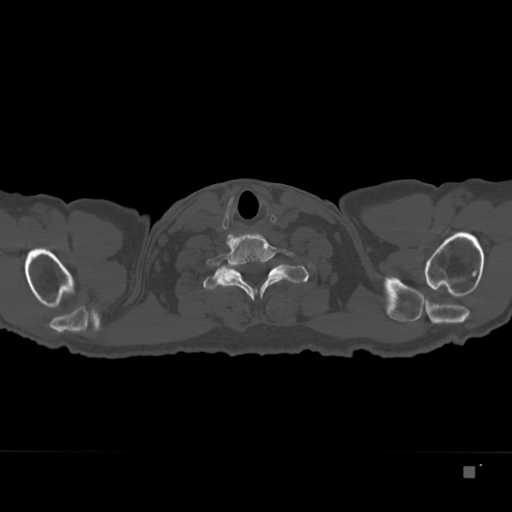
CT including the spine, one axial slice. 120 kVp. Bone window (W 1800 / L 400 HU). 1.5 mm slice thickness. 512 × 512 image matrix. Patient: male, 72 years. Case-level facts recorded for this patient, not image findings: primary cancer: skeletal.
Annotated regions visible in this slice (semi-automatically segmented with operator editing):
- T1 vertebra: bounding box (x1, y1, x2, y2) in pixels: (203, 264, 309, 295)